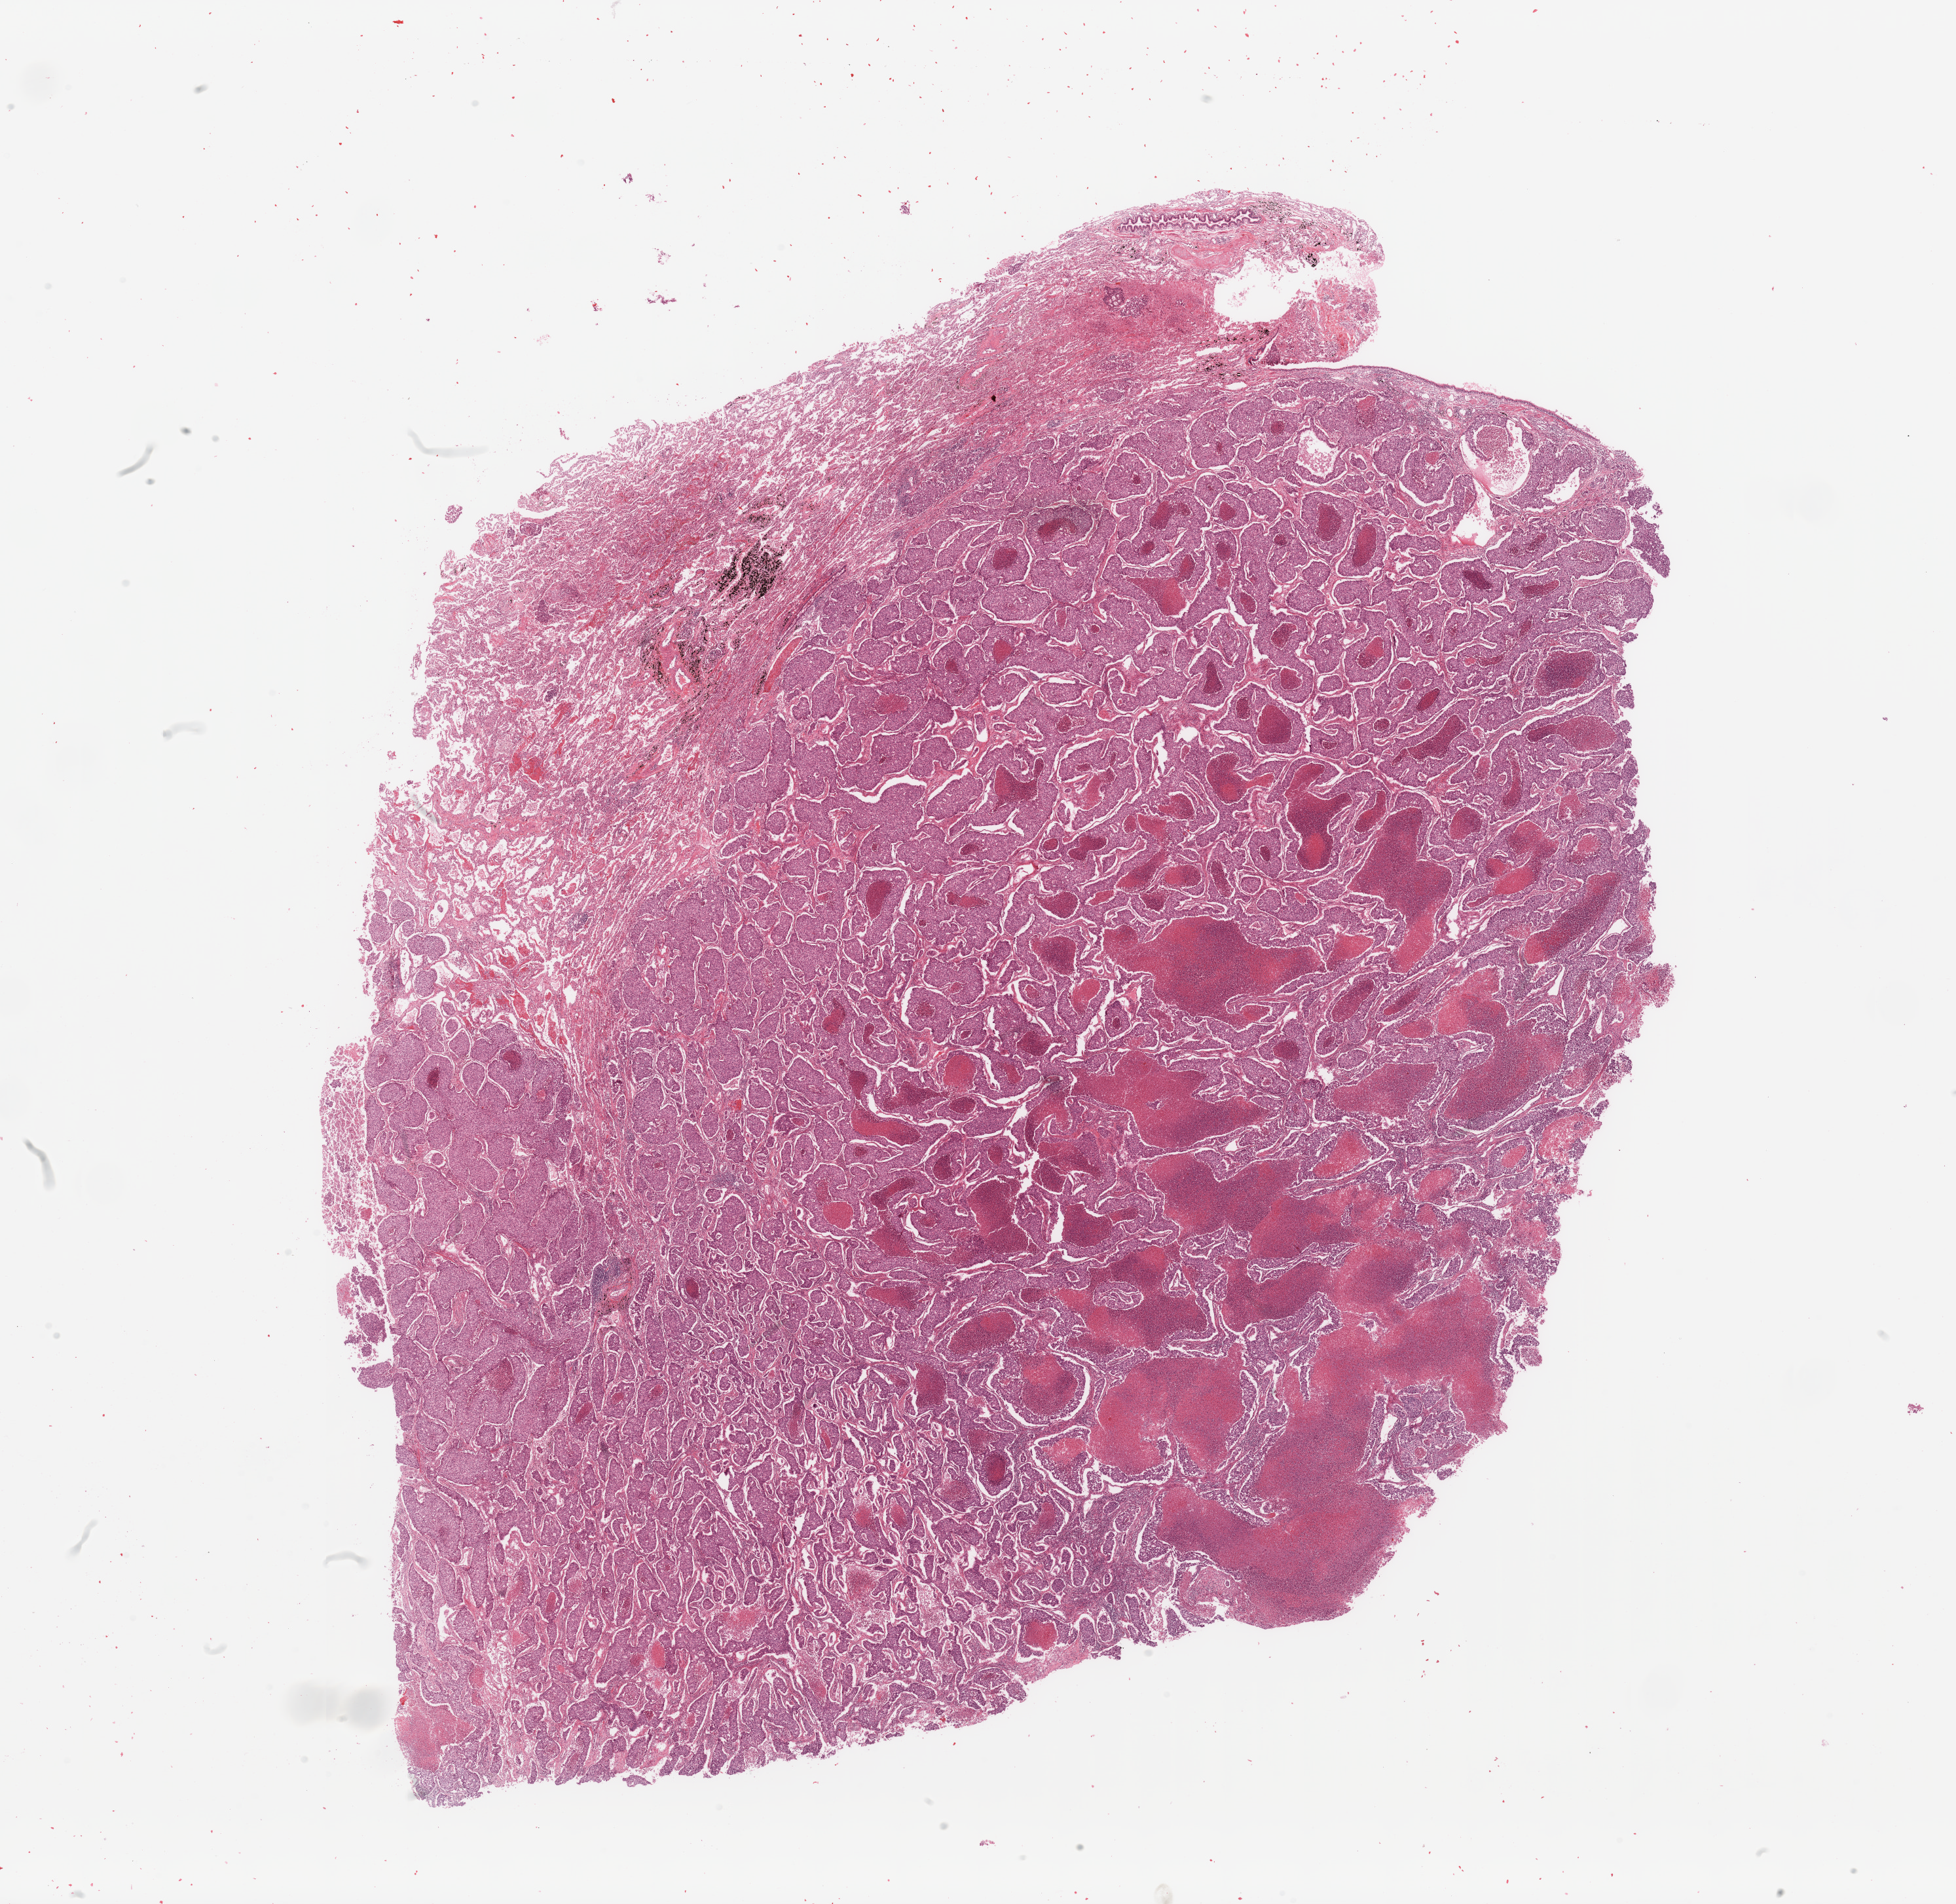
Whole-slide histology image, H&E — whole scanned area (about 23.6 x 23.0 mm, slide scanned at 20x) shown as a low-resolution overview. Tumour tissue sample, sampled site: lung. Patient: male, age 45 years. Histologic grade: G3 (poorly differentiated). Composition of this section per pathologist review: tumour nuclei 70%, necrosis 20%.
Diagnosis: Adenocarcinoma, NOS. AJCC pathologic stage: IIB.